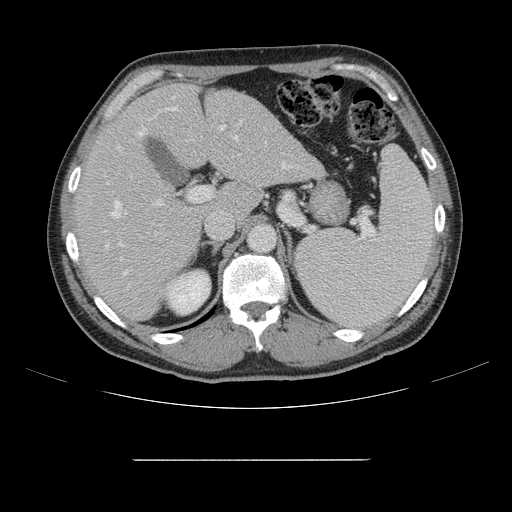
Contrast-enhanced abdominal CT, one axial slice. Position 98 of 164 along the scan axis. 120 kVp. Intravenous contrast given. Soft-tissue window (W 400 / L 40 HU). 2.5 mm slice thickness. 512 × 512 image matrix, field of view 404 × 404 mm. Male patient, age 54 years. From the clinical record (not read from this slice): diagnosis: colorectal cancer liver metastases, imaged before liver resection; multiple liver metastases: yes; largest metastasis: 1 cm; disease in both lobes: no.
Annotated regions visible in this slice (expert manual segmentation):
- hepatic veins: box from (x=105, y=132) to (x=286, y=276) px
- liver: (x=77, y=85)–(x=321, y=321)
- planned liver remnant (the part of the liver to remain after resection): (x=77, y=85)–(x=235, y=320)
- portal vein (with intrahepatic branches): (x=118, y=96)–(x=242, y=205)